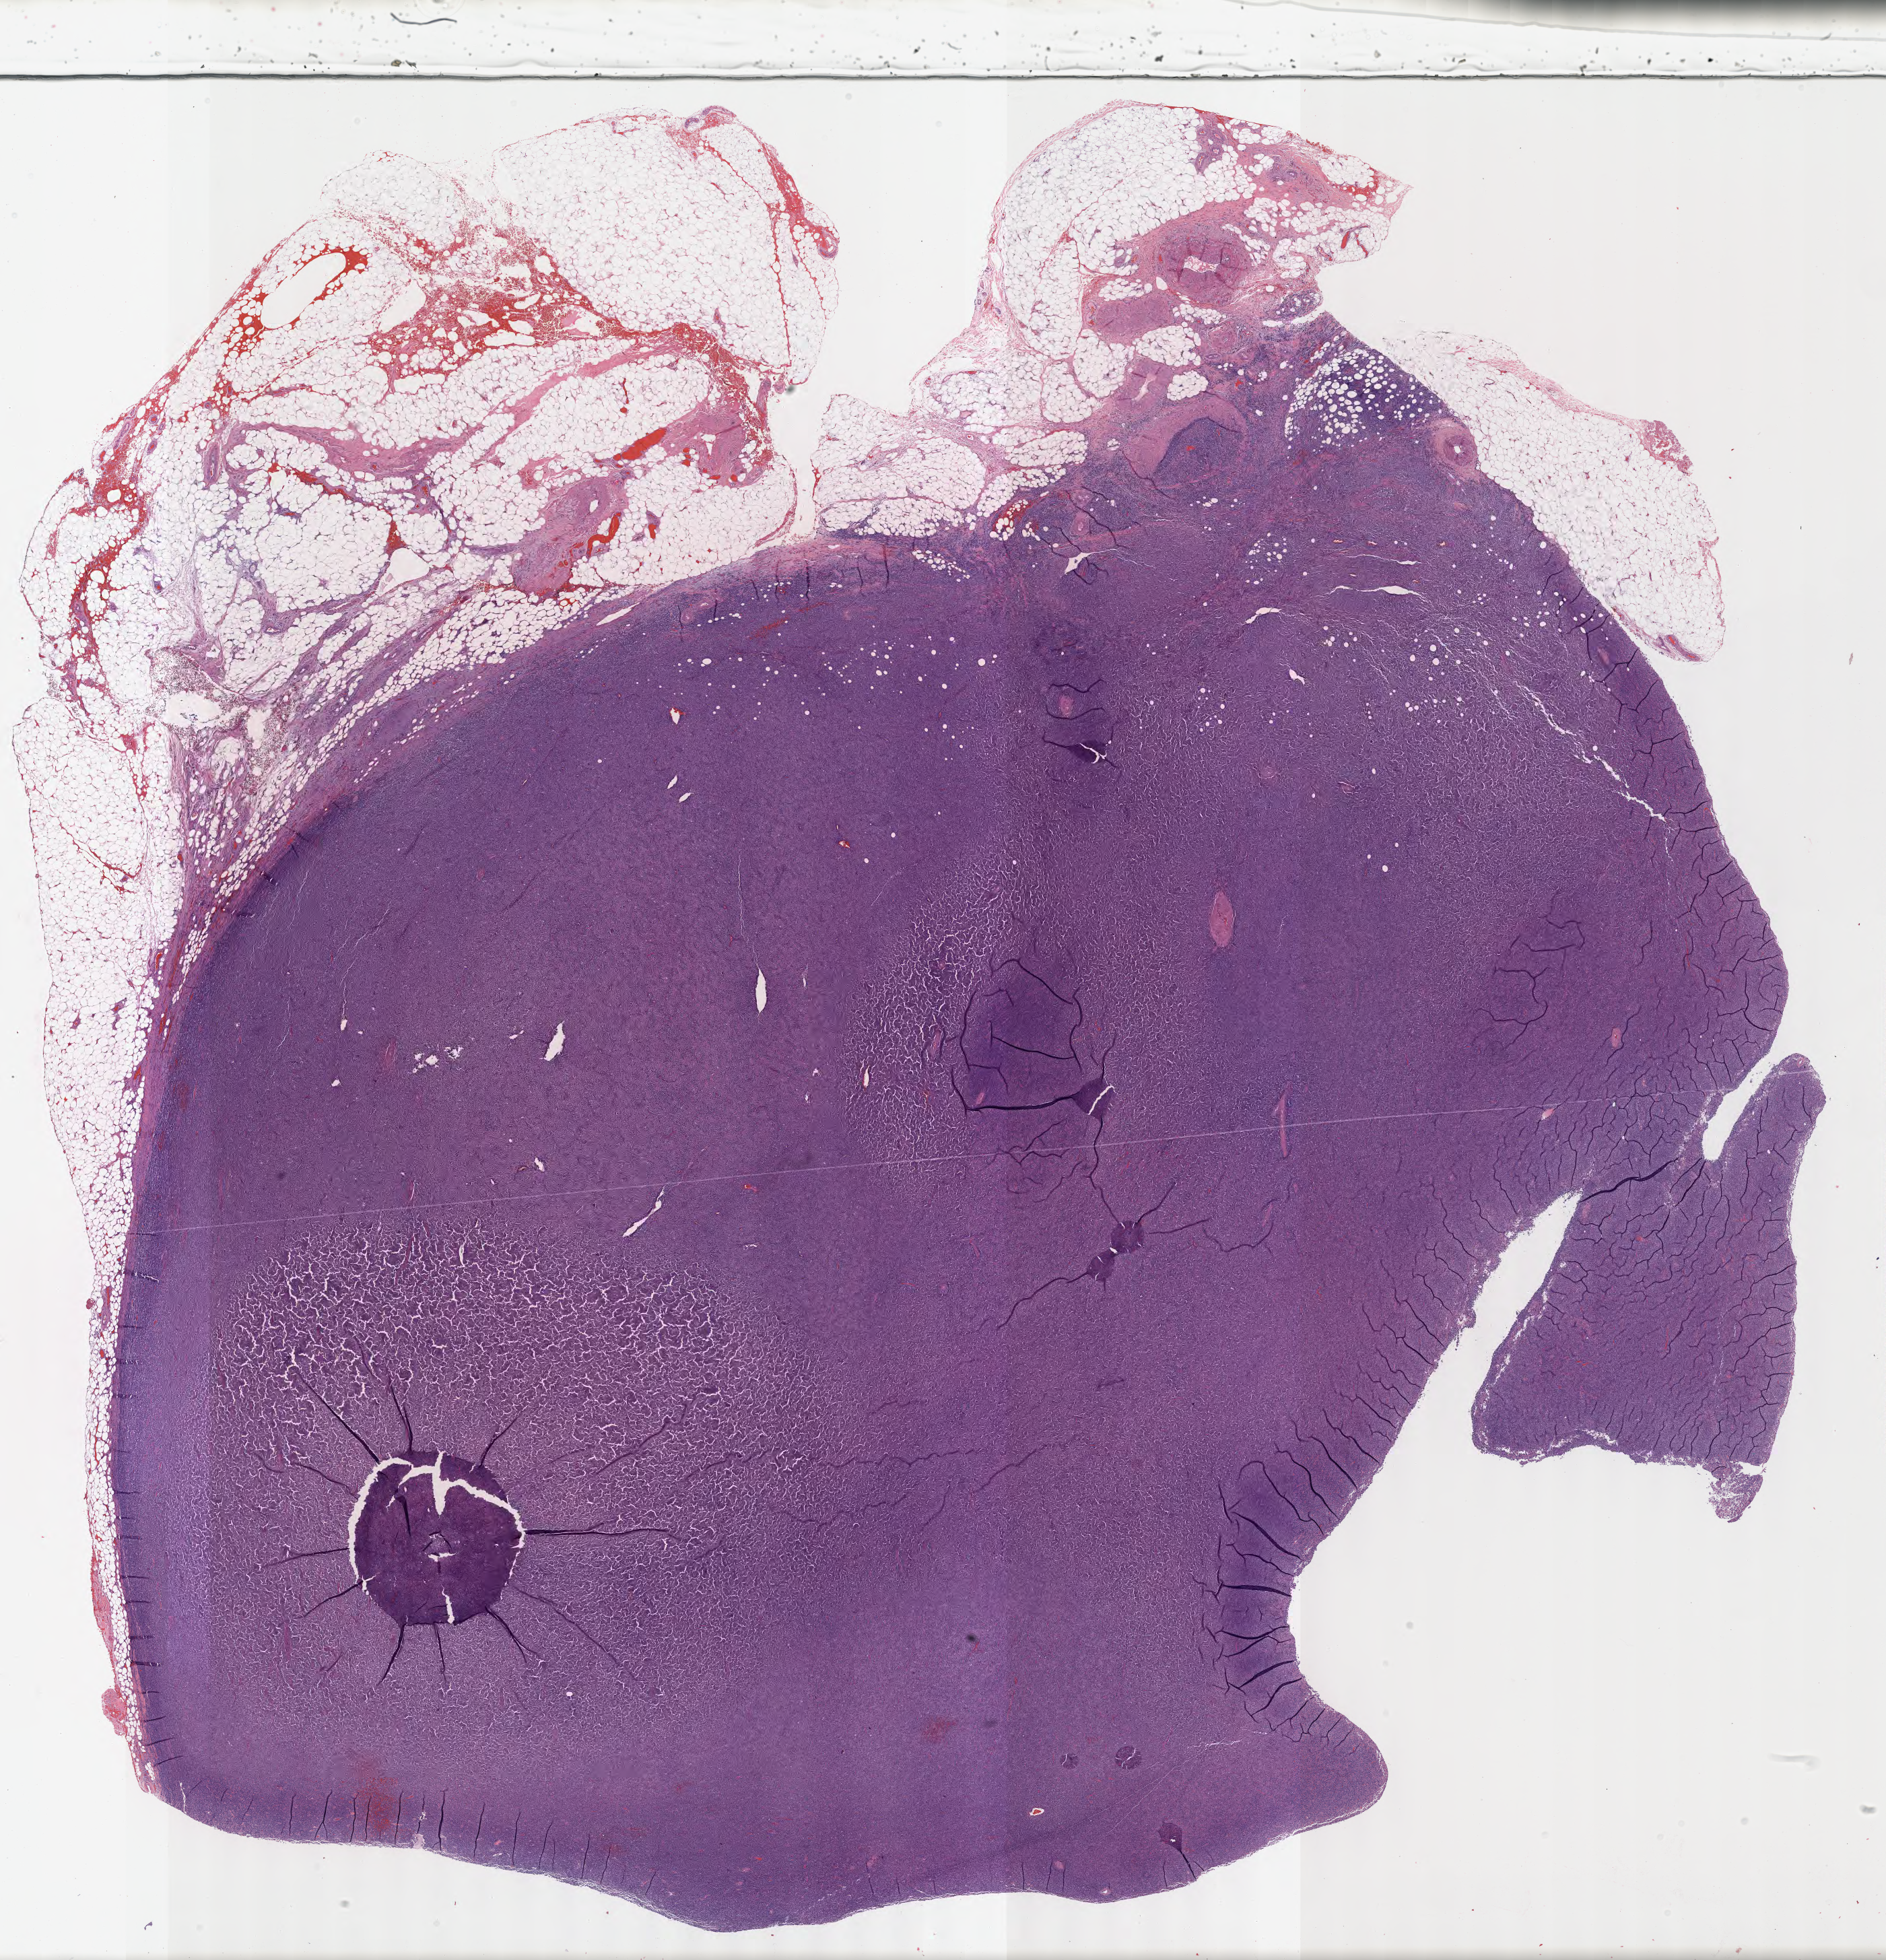
Digitized hematoxylin and eosin (H&E)-stained section — a low-resolution overview of the entire scanned area, about 22.6 x 23.5 mm. Tumor tissue. Anatomic site: lymph node. Male patient, age 54 years.
- histologic diagnosis: Diffuse large B-cell lymphoma, NOS